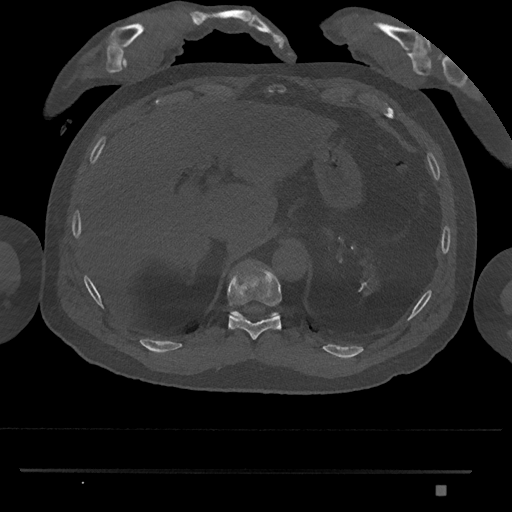
CT including the spine, one axial slice; position 991 of 1134 along the scan axis; reconstruction kernel Br40s/3; bone window (W 1800 / L 400 HU); 0.5 mm slice thickness; 512 × 512 image matrix. Patient: male, 65 years. Case-level facts recorded for this patient, not image findings: primary cancer: prostate.
Structures marked on this image (semi-automatic segmentation, software-assisted and operator-edited):
- T10 vertebra: bounding box [x1, y1, x2, y2] px = [228, 264, 282, 340]
- T11 vertebra: [230, 310, 279, 318]